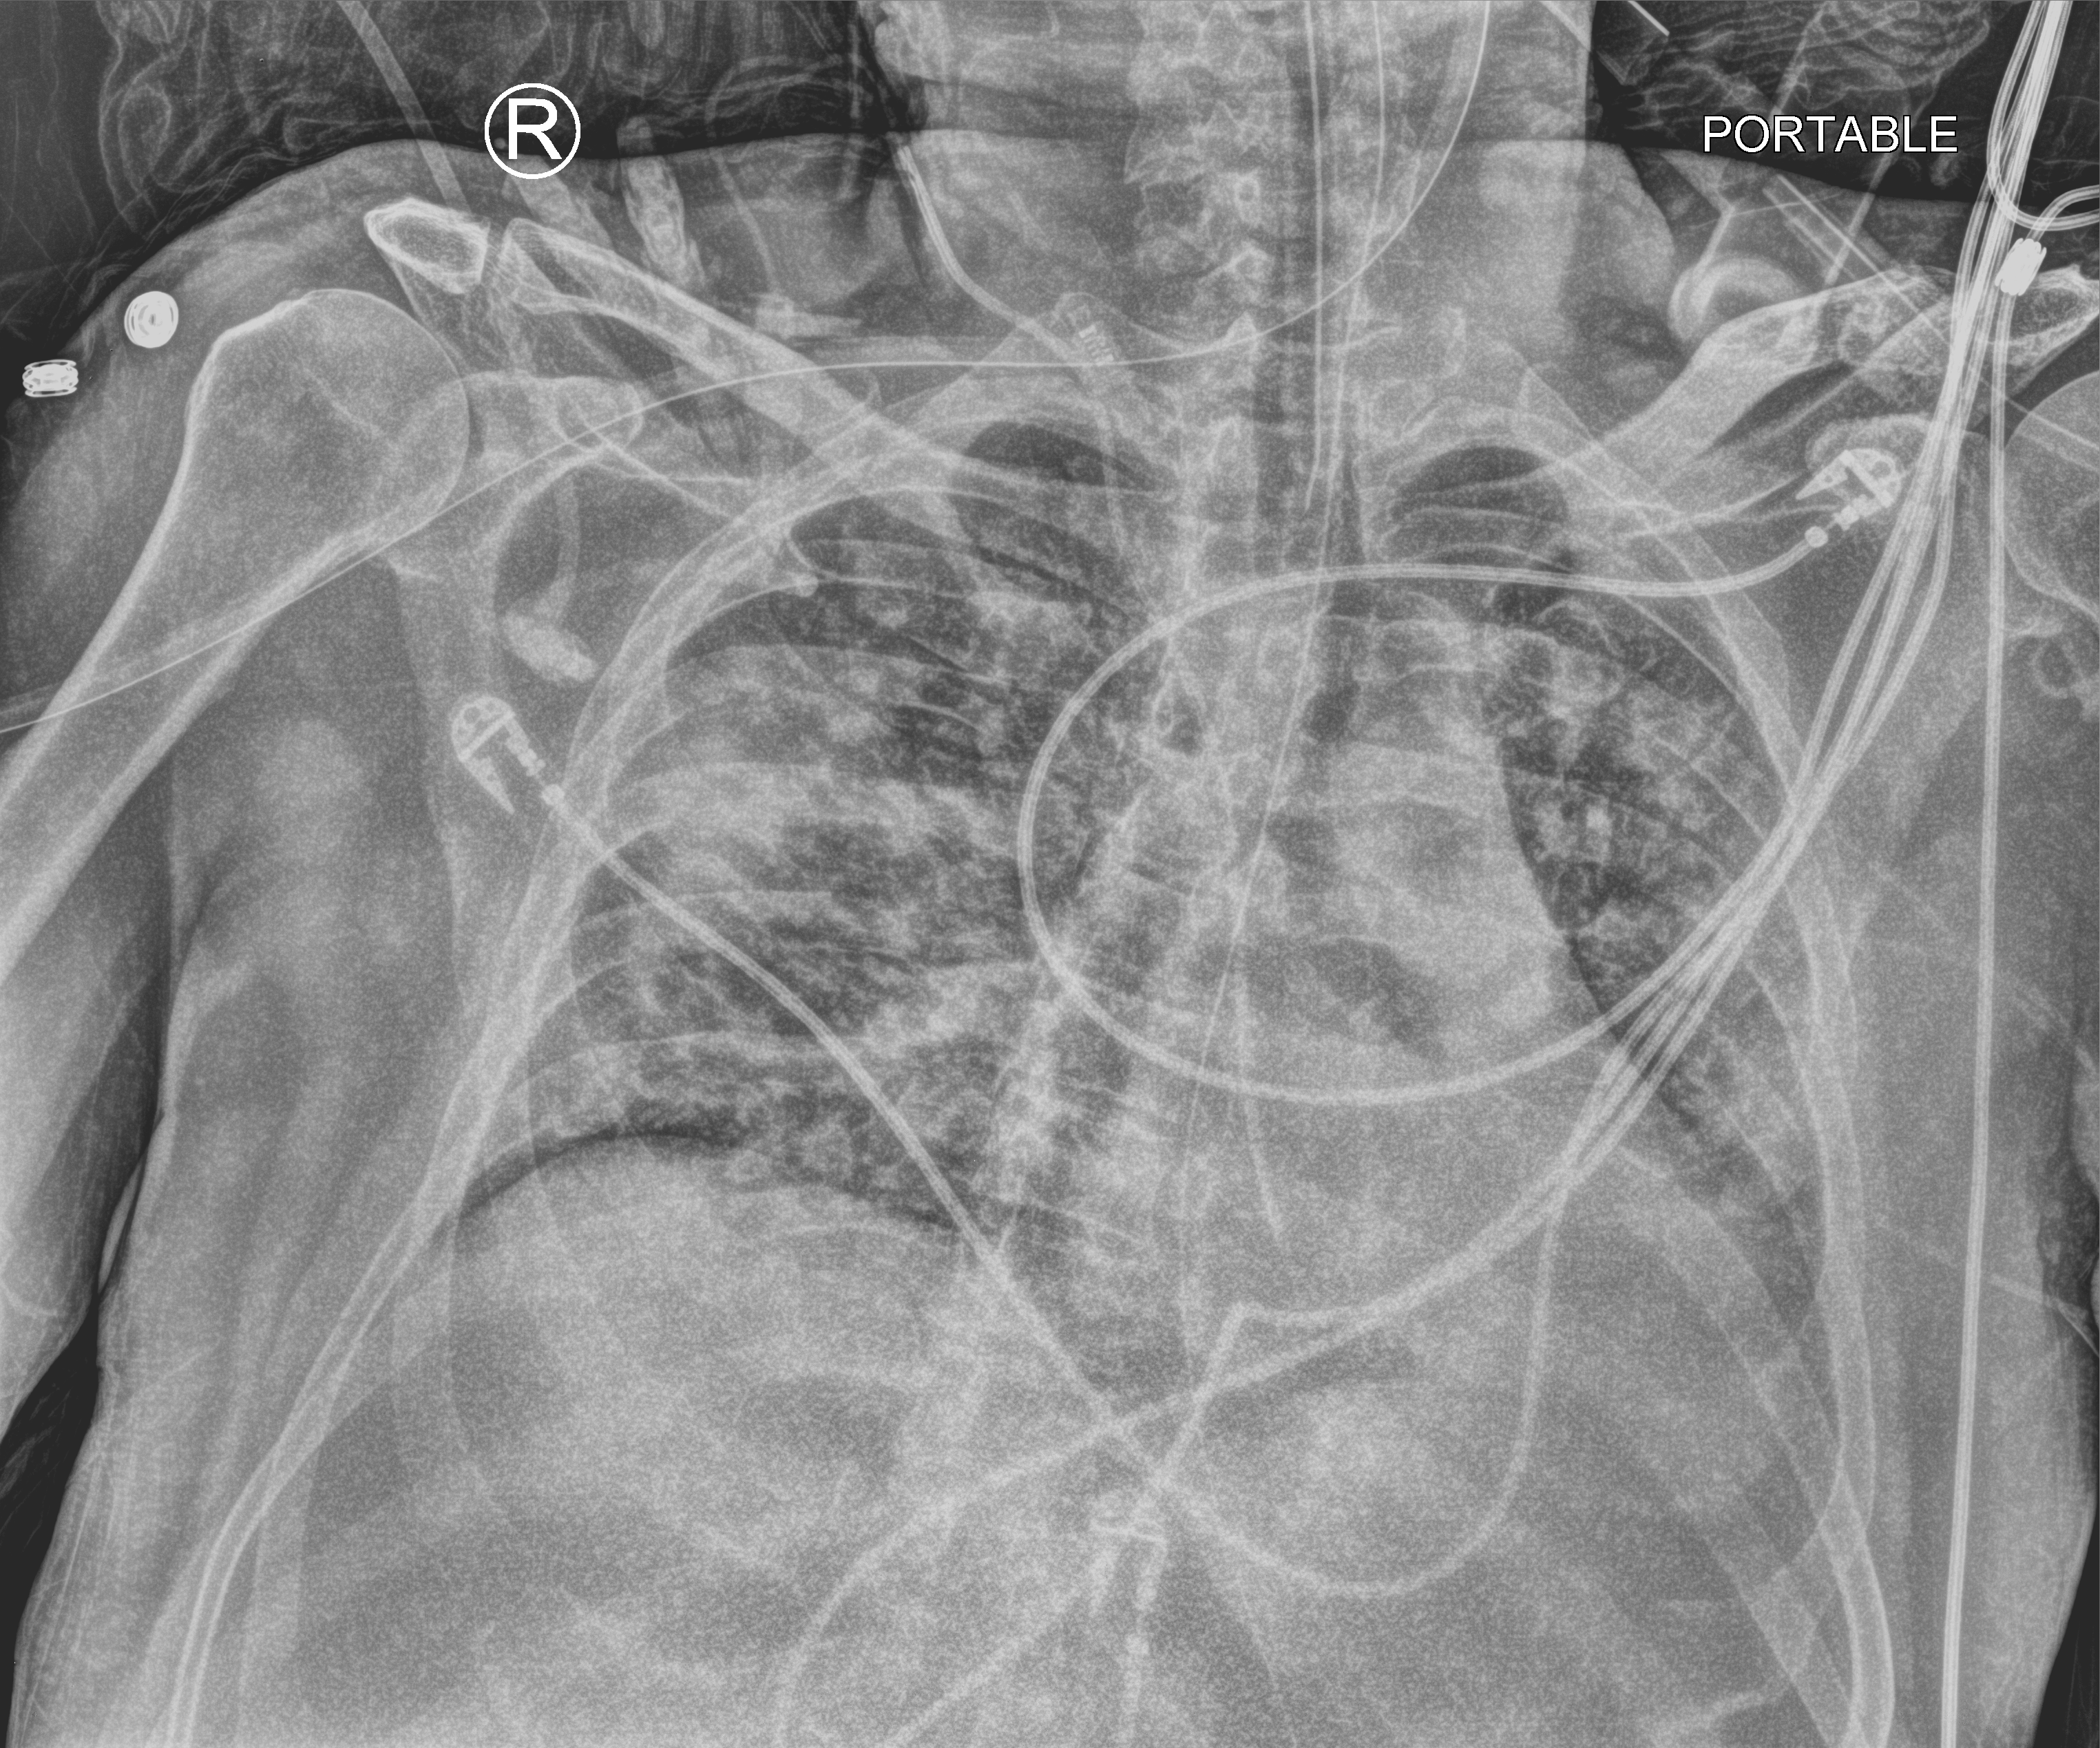
Bedside chest radiograph (computed radiography), anteroposterior (AP) projection. Male patient hospitalised with COVID-19, age 18–59 years.
Admission-level facts for this patient (not findings on this image; timing relative to this image not recorded): length of hospital stay: 25 days.